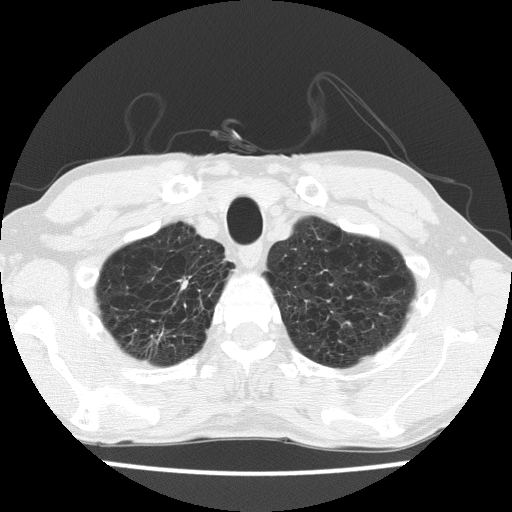
Chest CT (low-dose screening protocol), one axial image. Second screening round (one year after baseline). Lung window (W 1500 / L -600 HU). 2 mm slice thickness. Male participant, aged 63 years at enrolment. Current smoker at enrolment.
Expert reader's lesion annotation, bounding box (x1, y1, x2, y2) in pixels: (136, 260, 203, 331). Screening reader's record for this exam: no non-calcified nodule ≥4 mm recorded.